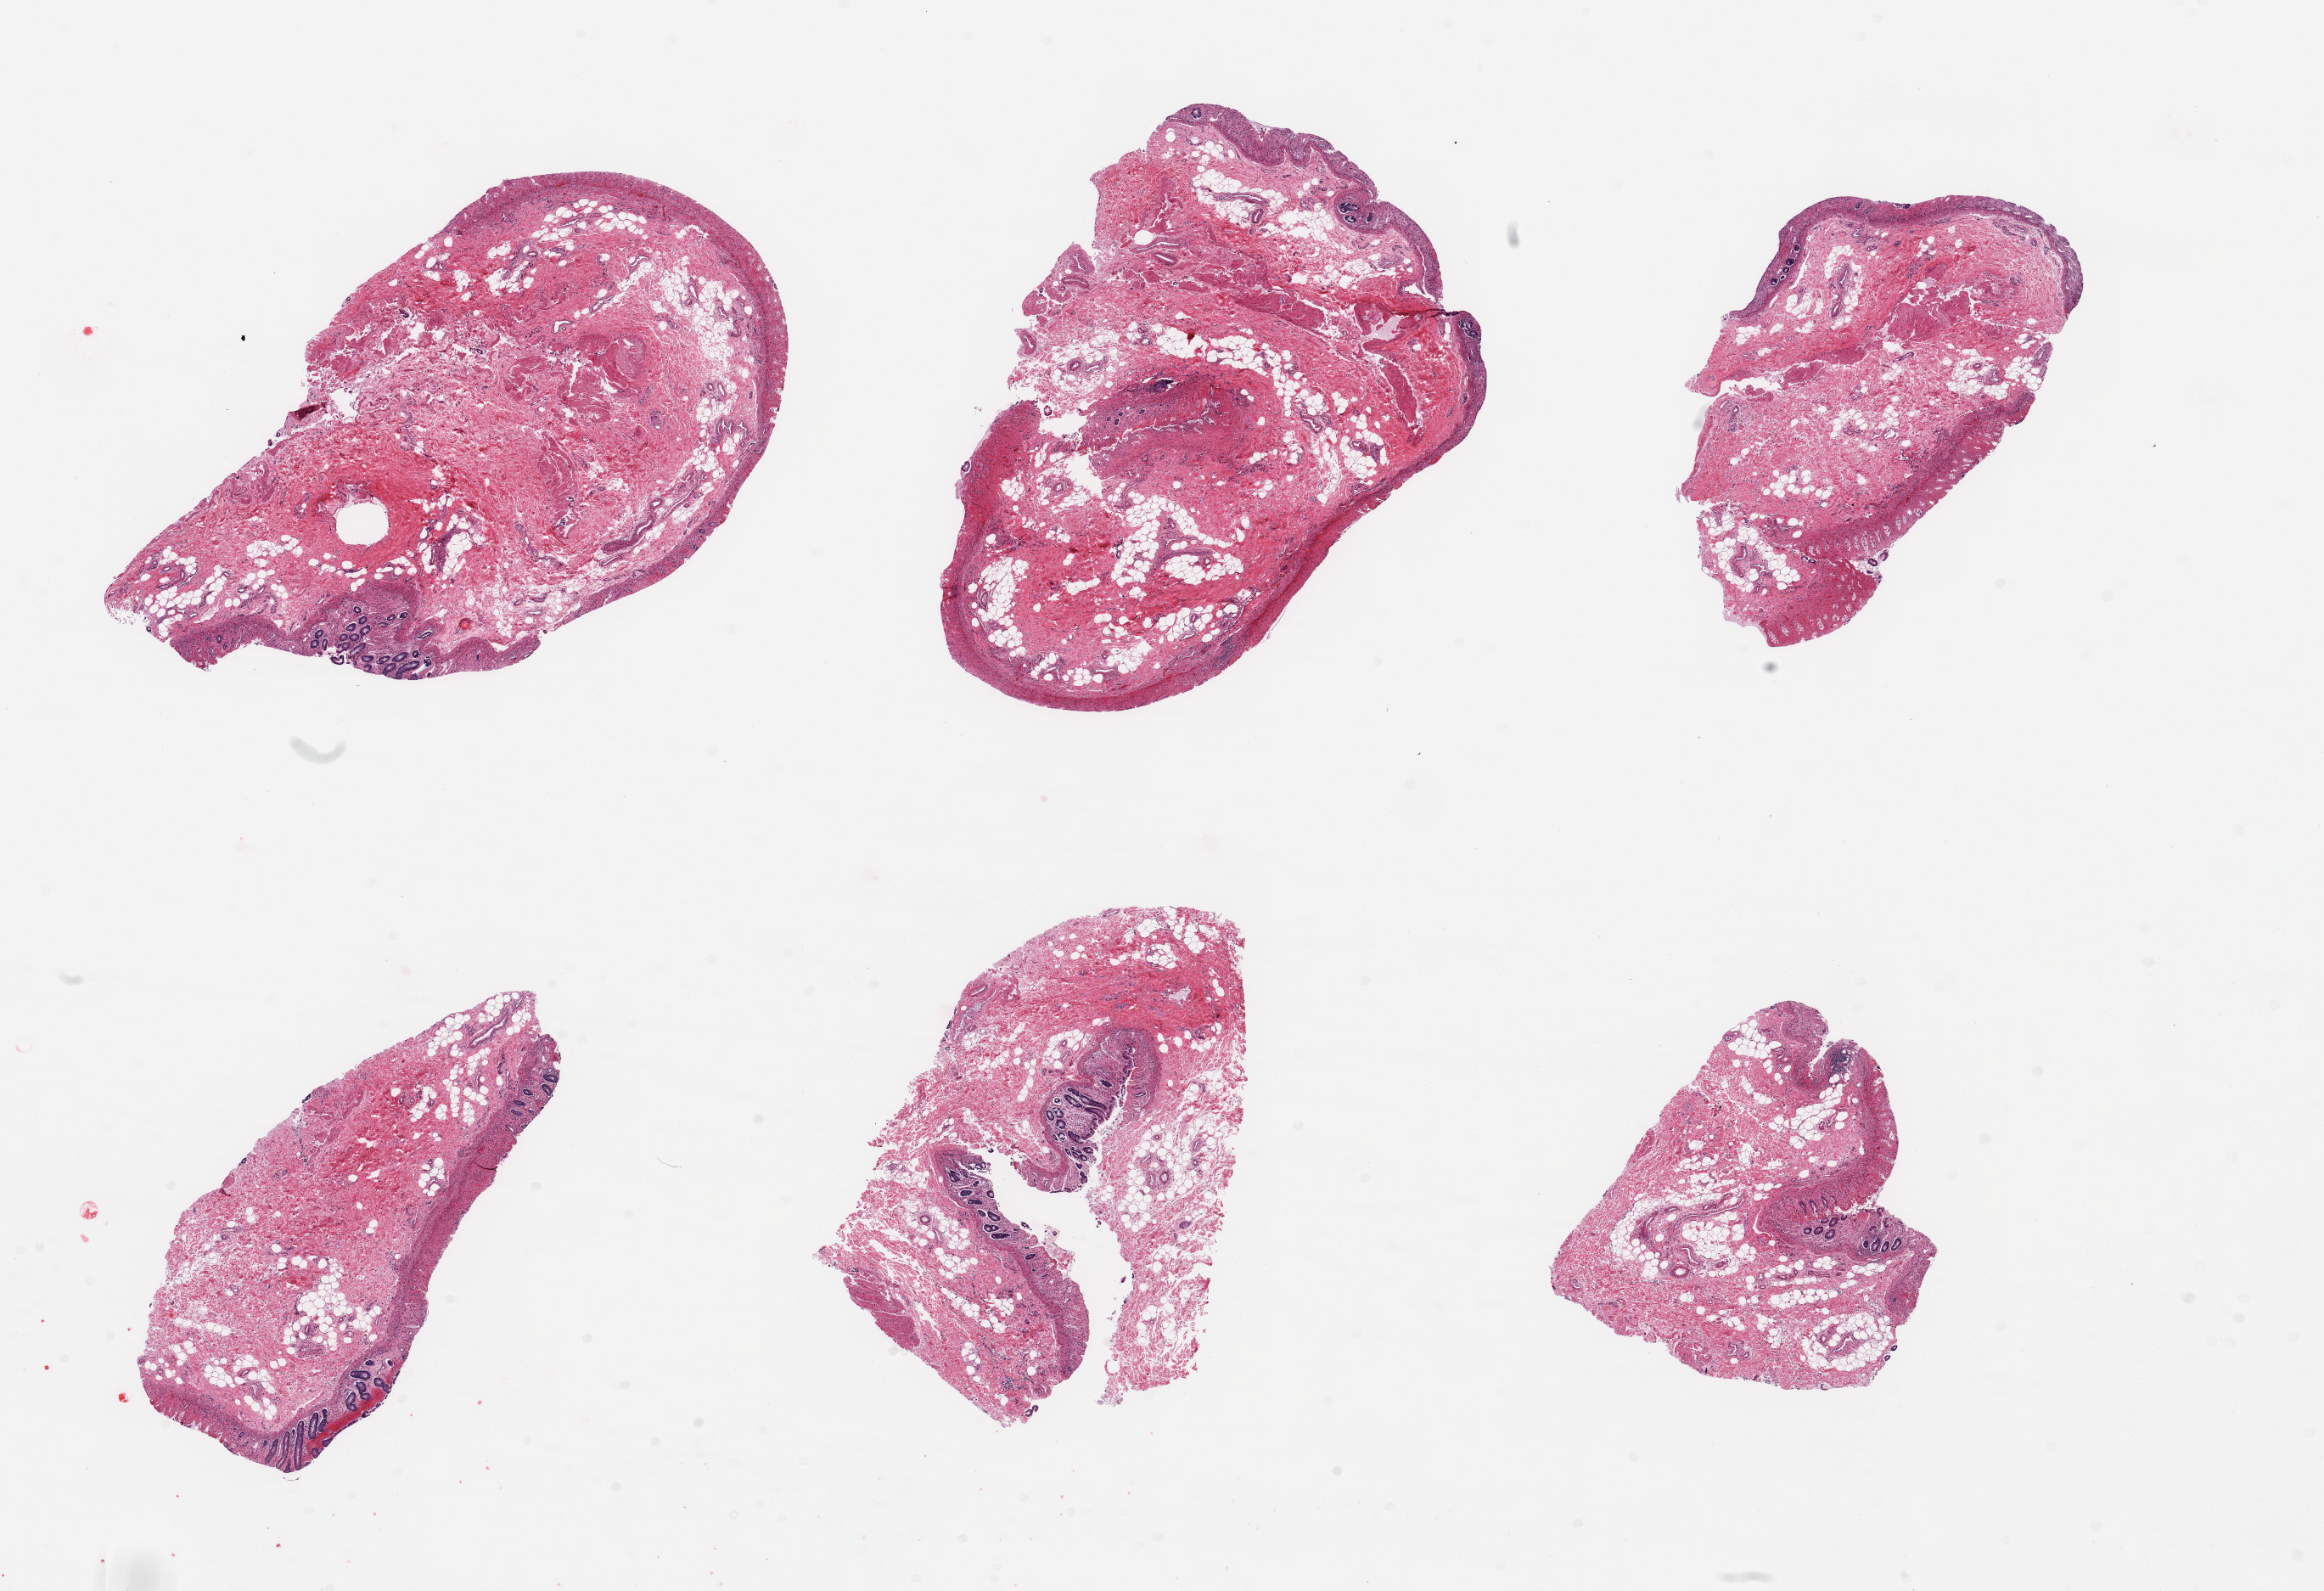
Hematoxylin and eosin (H&E) whole-slide image, brightfield — a low-resolution overview of the entire scanned area, about 21.7 x 14.8 mm, PAXgene-fixed paraffin-embedded (PFPE) section, sampled site (target tissue): sigmoid colon, donor tissue sample.
Pathologist's review note for this sample: 6 pieces; severely autolyzed mucosa and lack of good representation of target muscularis.